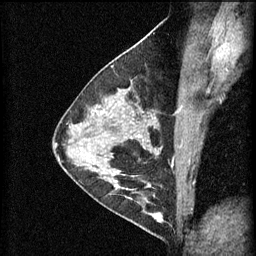
Breast MRI (dynamic contrast-enhanced), one sagittal slice. Position 35 of 60 along the scan axis. 3 images stored at this slice position (order not interpretable as contrast timing). 1.5 T. TE 4.2 ms, TR 11 ms. 2 mm slice thickness. 256 × 256 image matrix, field of view 180 × 180 mm. Patient: female, 29 years.
Outlined on this slice (semi-automatically segmented with operator editing):
- analysis volume of interest (the breast-tissue region the enhancement analysis was run in; not a lesion): bounding box <105,172,166,227> (left, top, right, bottom; pixels)
- tumour enhancement mask (voxels above the 70 % enhancement threshold inside the analysis volume of interest): <105,172,164,223>